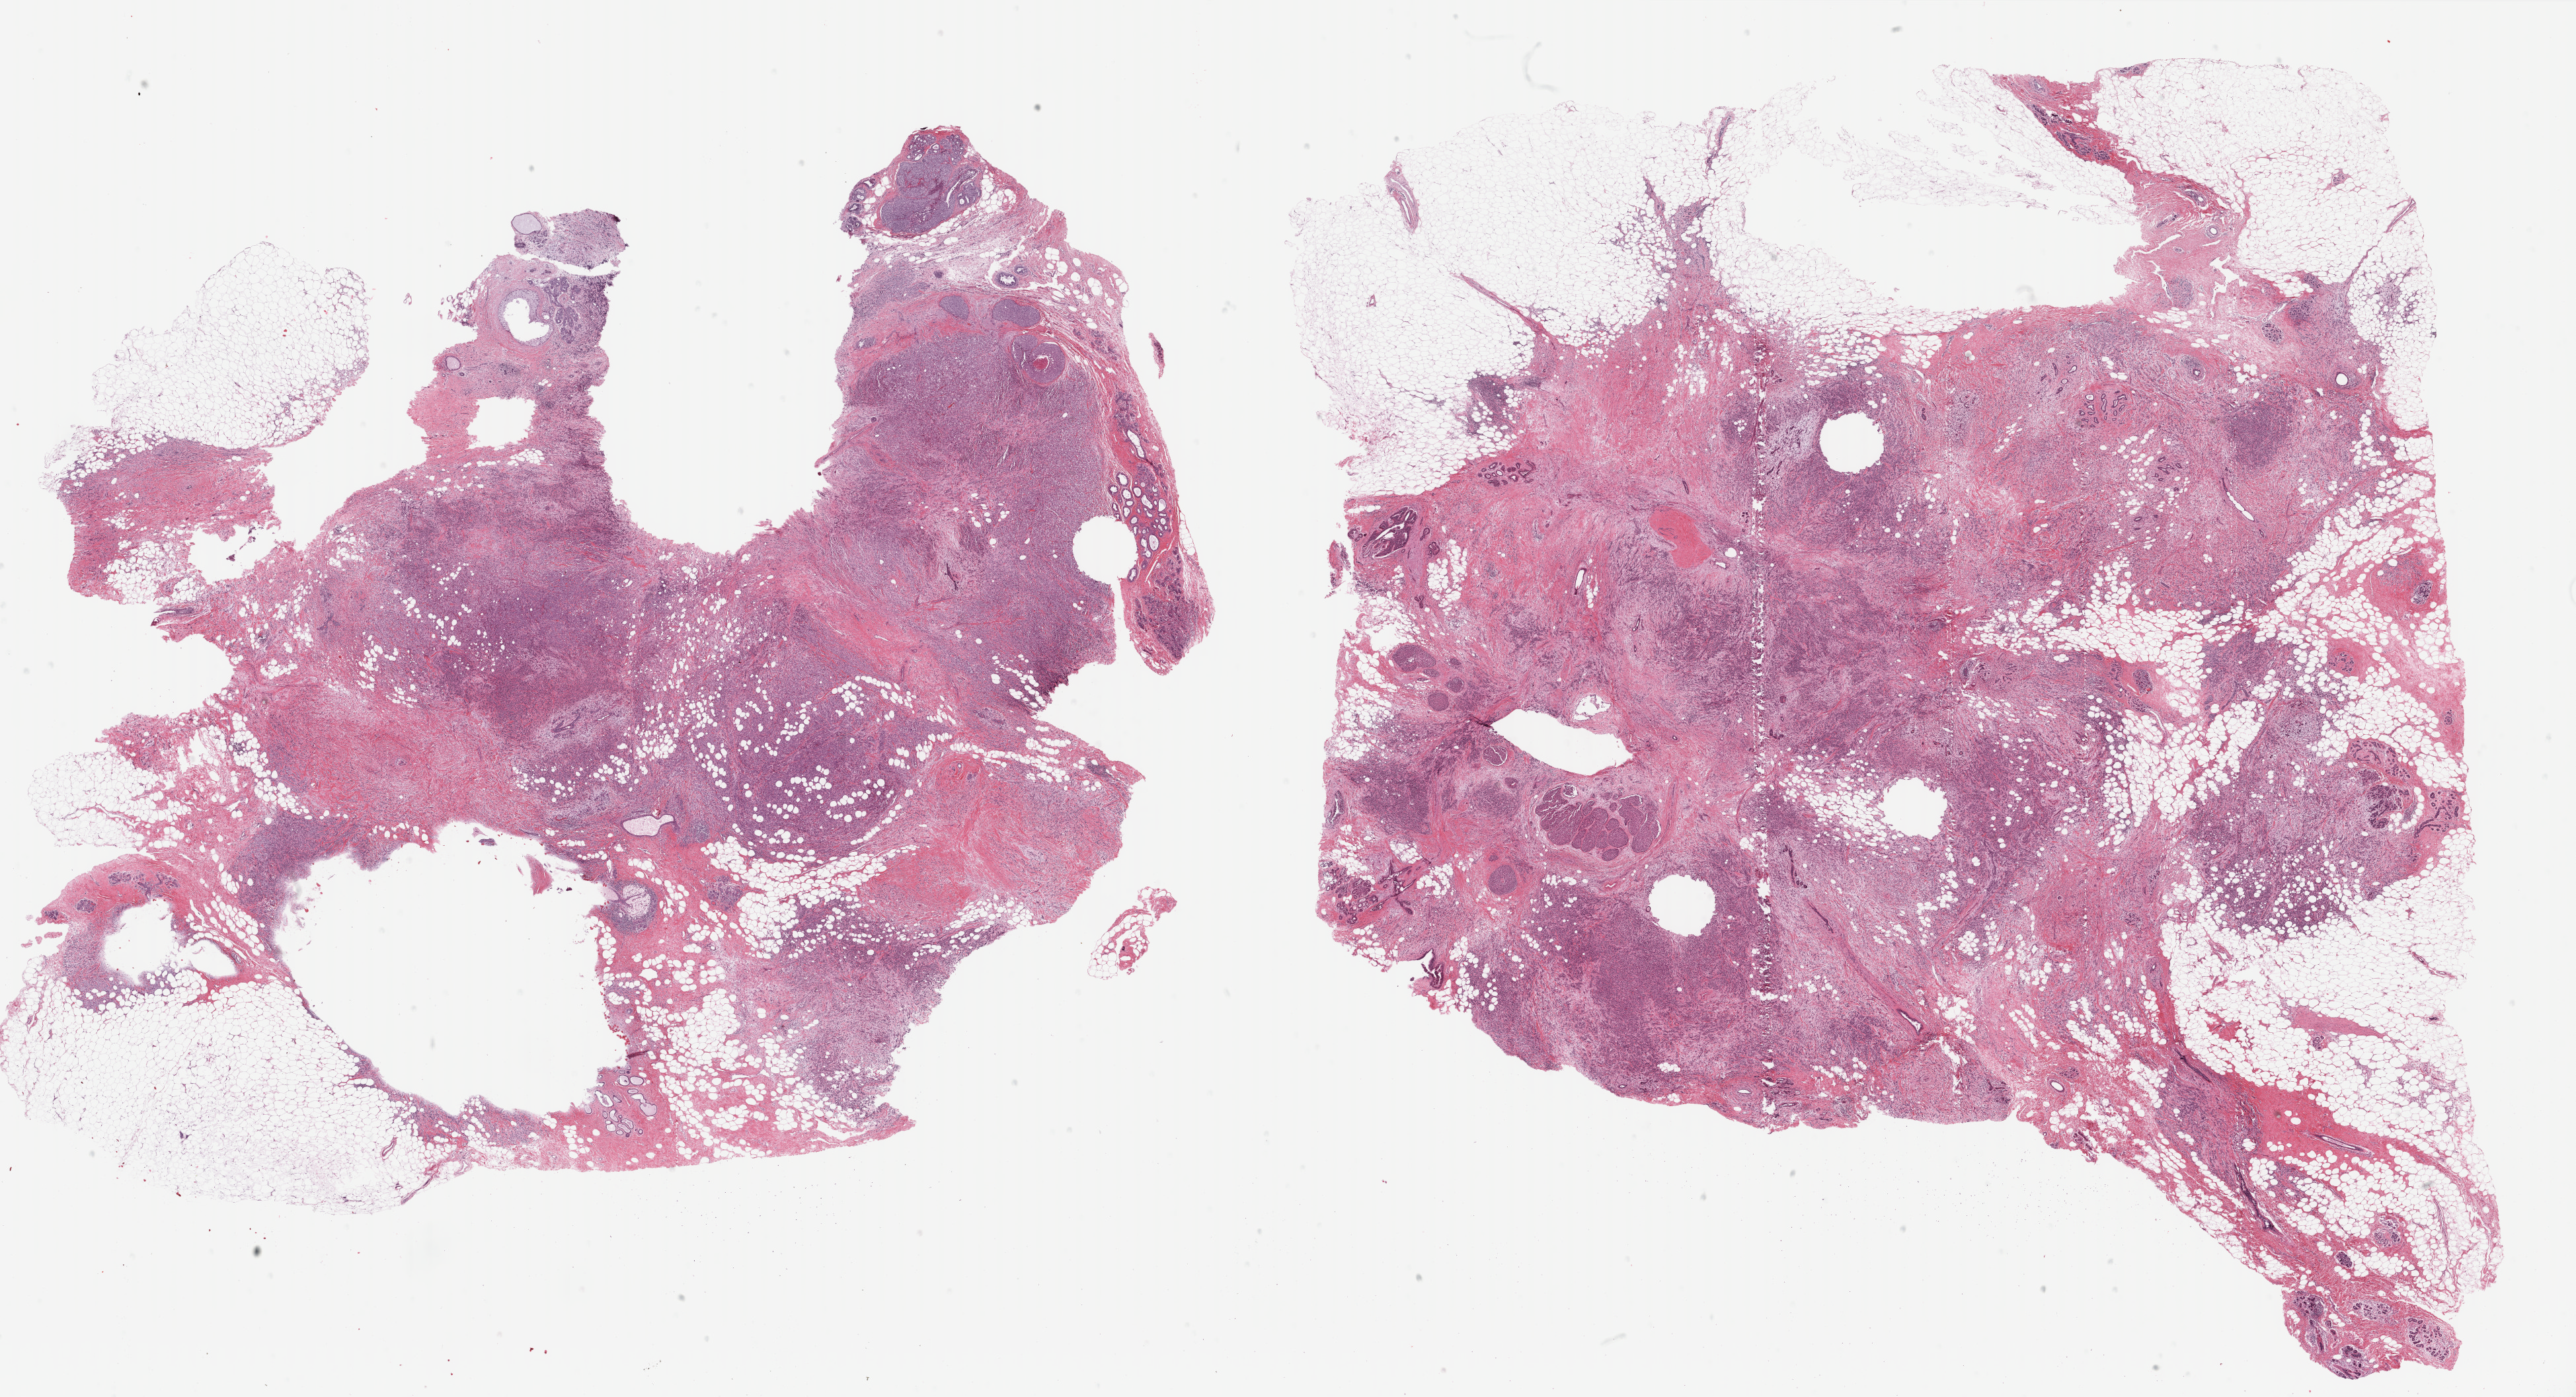
Digitized H&E tissue section (whole slide), whole scanned area (about 30.9 x 16.8 mm) shown as a low-resolution overview; FFPE section; breast, primary tumour sample. Female, age 40 years at initial diagnosis.
AJCC pathologic stage: IIIA (6th edition). Lymph nodes positive (case pathology): 1 of 18 examined. Diagnosis: Lobular carcinoma, NOS.